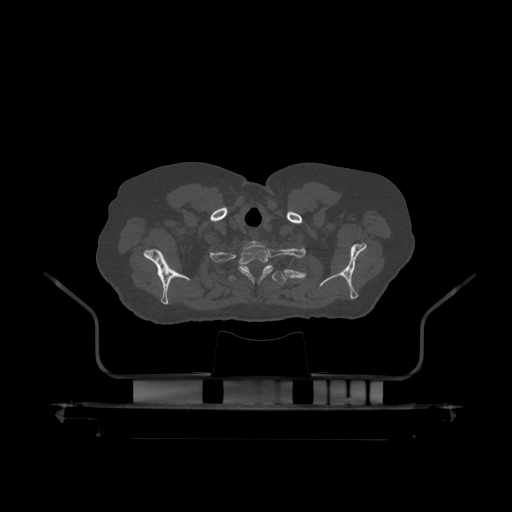
CT including the spine, one axial slice. Bone window (W 1800 / L 400 HU). 1.25 mm slice thickness. 512 × 512 image matrix, field of view 650 × 650 mm. Male patient, age 60 years. From the clinical record (not read from this slice): primary cancer: prostate.
Structures marked on this image (semi-automatic segmentation, software-assisted and operator-edited):
- T1 vertebra: box from (x=239, y=241) to (x=274, y=282) px
- T2 vertebra: (x=228, y=266)–(x=287, y=284)